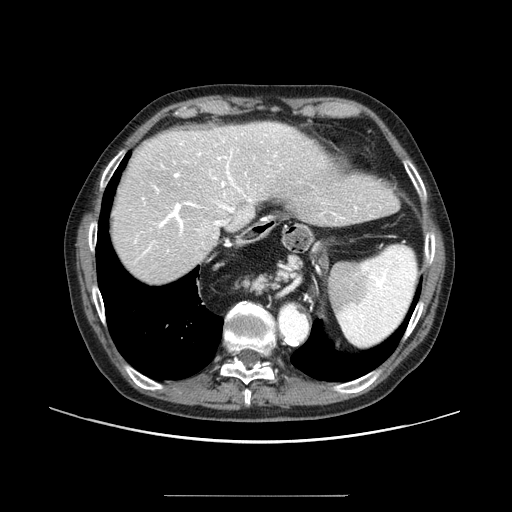
Contrast-enhanced abdominal CT (liver protocol), one axial slice. Slice 71 of 91 in the series (ordered by position). Reconstruction kernel STANDARD. 100 kVp. One of 2 acquisitions stored at this slice position. Soft-tissue window (W 400 / L 40 HU). 2.5 mm slice thickness. 512 × 512 image matrix, field of view 400 × 400 mm. From the clinical record (not read from this slice): diagnosis: hepatocellular carcinoma (patient treated with transarterial chemoembolisation; whether this scan precedes or follows treatment is not stated here); TNM stage (as recorded): Stage-I; Child-Pugh class: A; tumour differentiation: moderately differentiated.
Structures marked on this image (semi-automatic segmentation, software-assisted and operator-edited):
- abdominal aorta: bounding box [x1, y1, x2, y2] px = [279, 306, 307, 341]
- liver parenchyma outside the tumour (the mass and vessels are separate outlines, so this box may not span the whole liver): [112, 122, 338, 282]
- liver vessels: [134, 125, 288, 254]